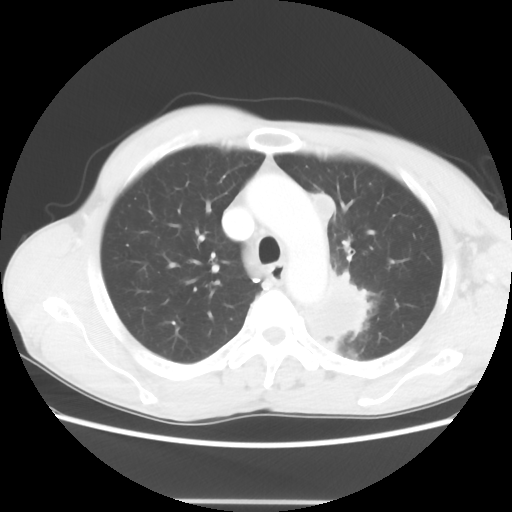
Chest CT, one axial slice. Position 48 of 62 along the scan axis. Reconstruction kernel STANDARD. Lung window (W 1500 / L -600 HU). 512 × 512 image matrix, field of view 360 × 360 mm. Patient: male, 61 years. From the clinical record (not read from this slice): clinical TNM (as recorded): T3 N1 M1.
Annotated regions visible in this slice (bounding box drawn by a radiologist):
- lung tumour (recorded histology: adenocarcinoma): bounding box [x1, y1, x2, y2] px = [289, 260, 372, 352]
- lung tumour (recorded histology: adenocarcinoma): [305, 186, 350, 227]